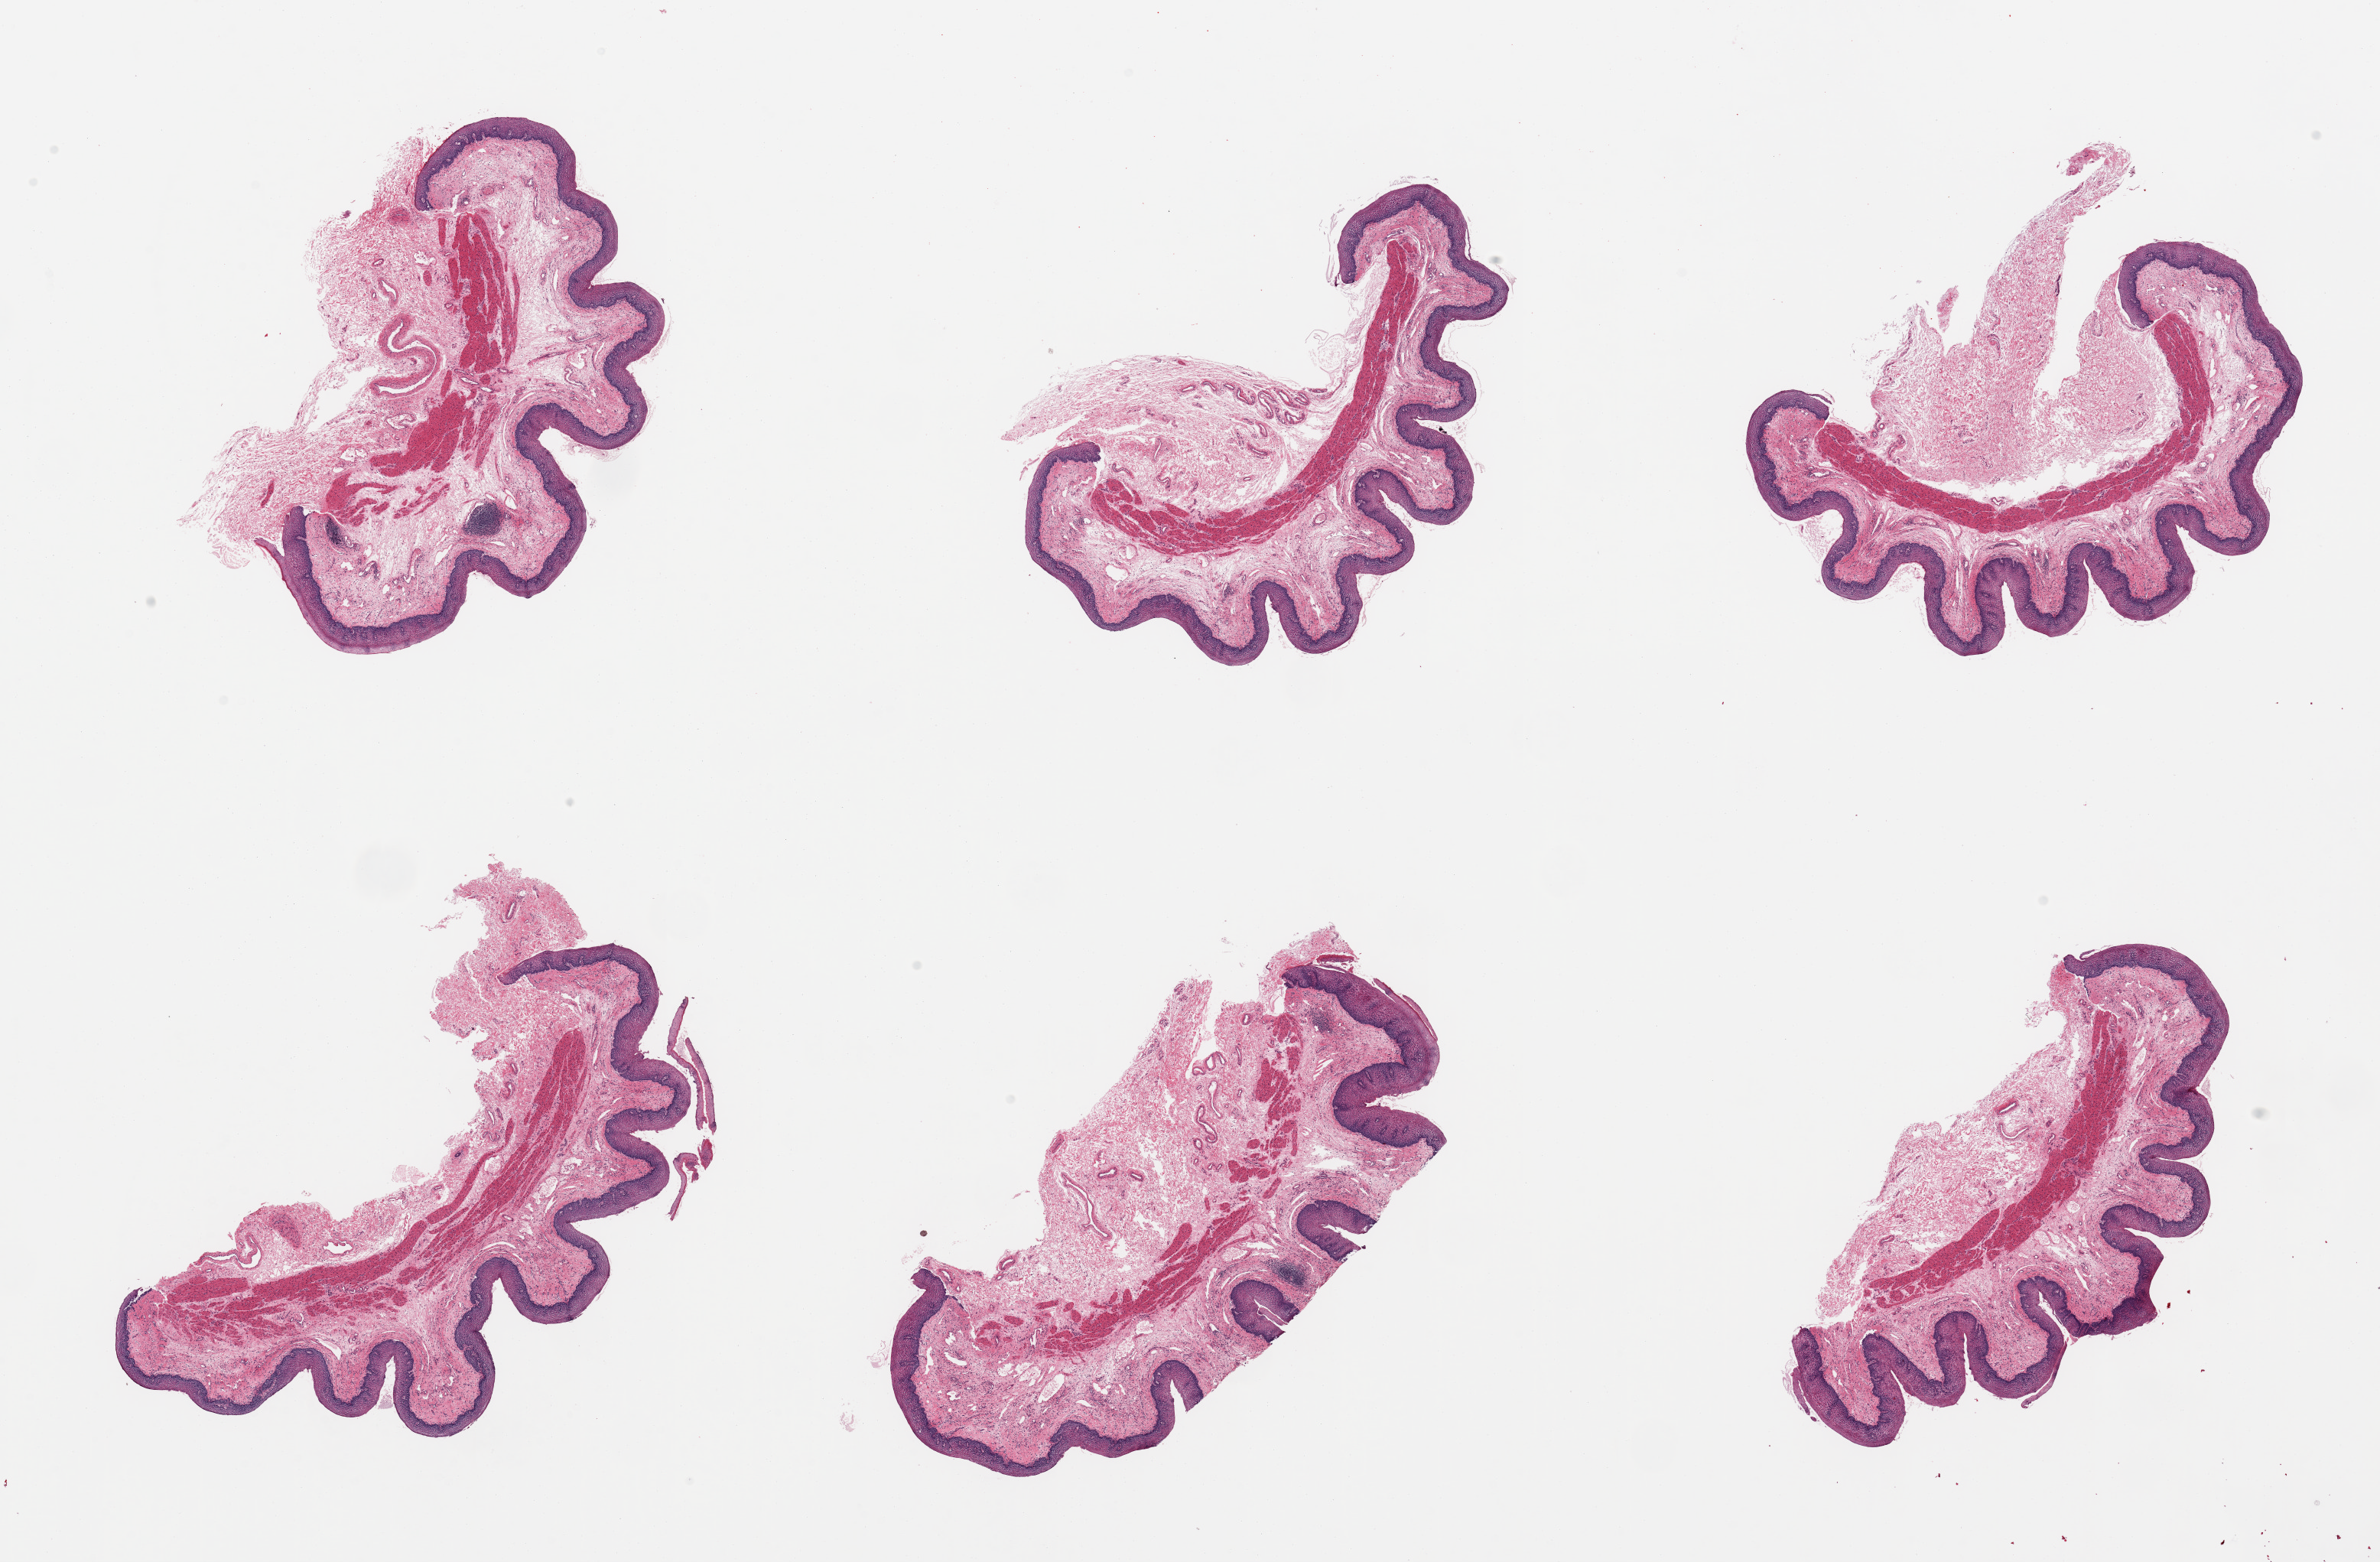
H&E whole-slide image, a low-resolution overview of the entire scanned area, about 24.6 x 16.1 mm; PAXgene-fixed paraffin-embedded (PFPE) section; section of esophageal mucous membrane (target tissue); donor tissue sample. Donor sex: female.
Reviewer comment on this tissue sample: 6 pieces, squamous mucosa is ~0.2-0.3mm.